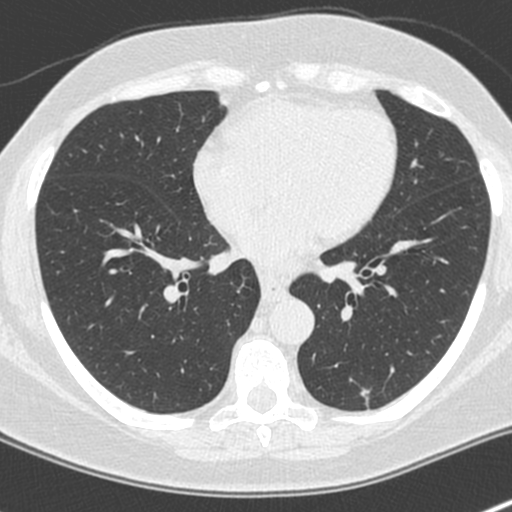
Low-dose screening chest CT, axial slice, first (baseline) screen, lung window (W 1500 / L -600 HU), 512 × 512 image matrix. Female, age 64 years at enrolment.
Lesion marked by an expert reader, bounding box [x1, y1, x2, y2] px = [345, 372, 394, 420]. Screening reader's record for this exam: no non-calcified nodule ≥4 mm recorded. Lung cancer was diagnosed 549 days after this screen: adenocarcinoma, NOS, left lower lobe, poorly differentiated (G3), stage IA (AJCC 6th edition), 8 mm at pathology.